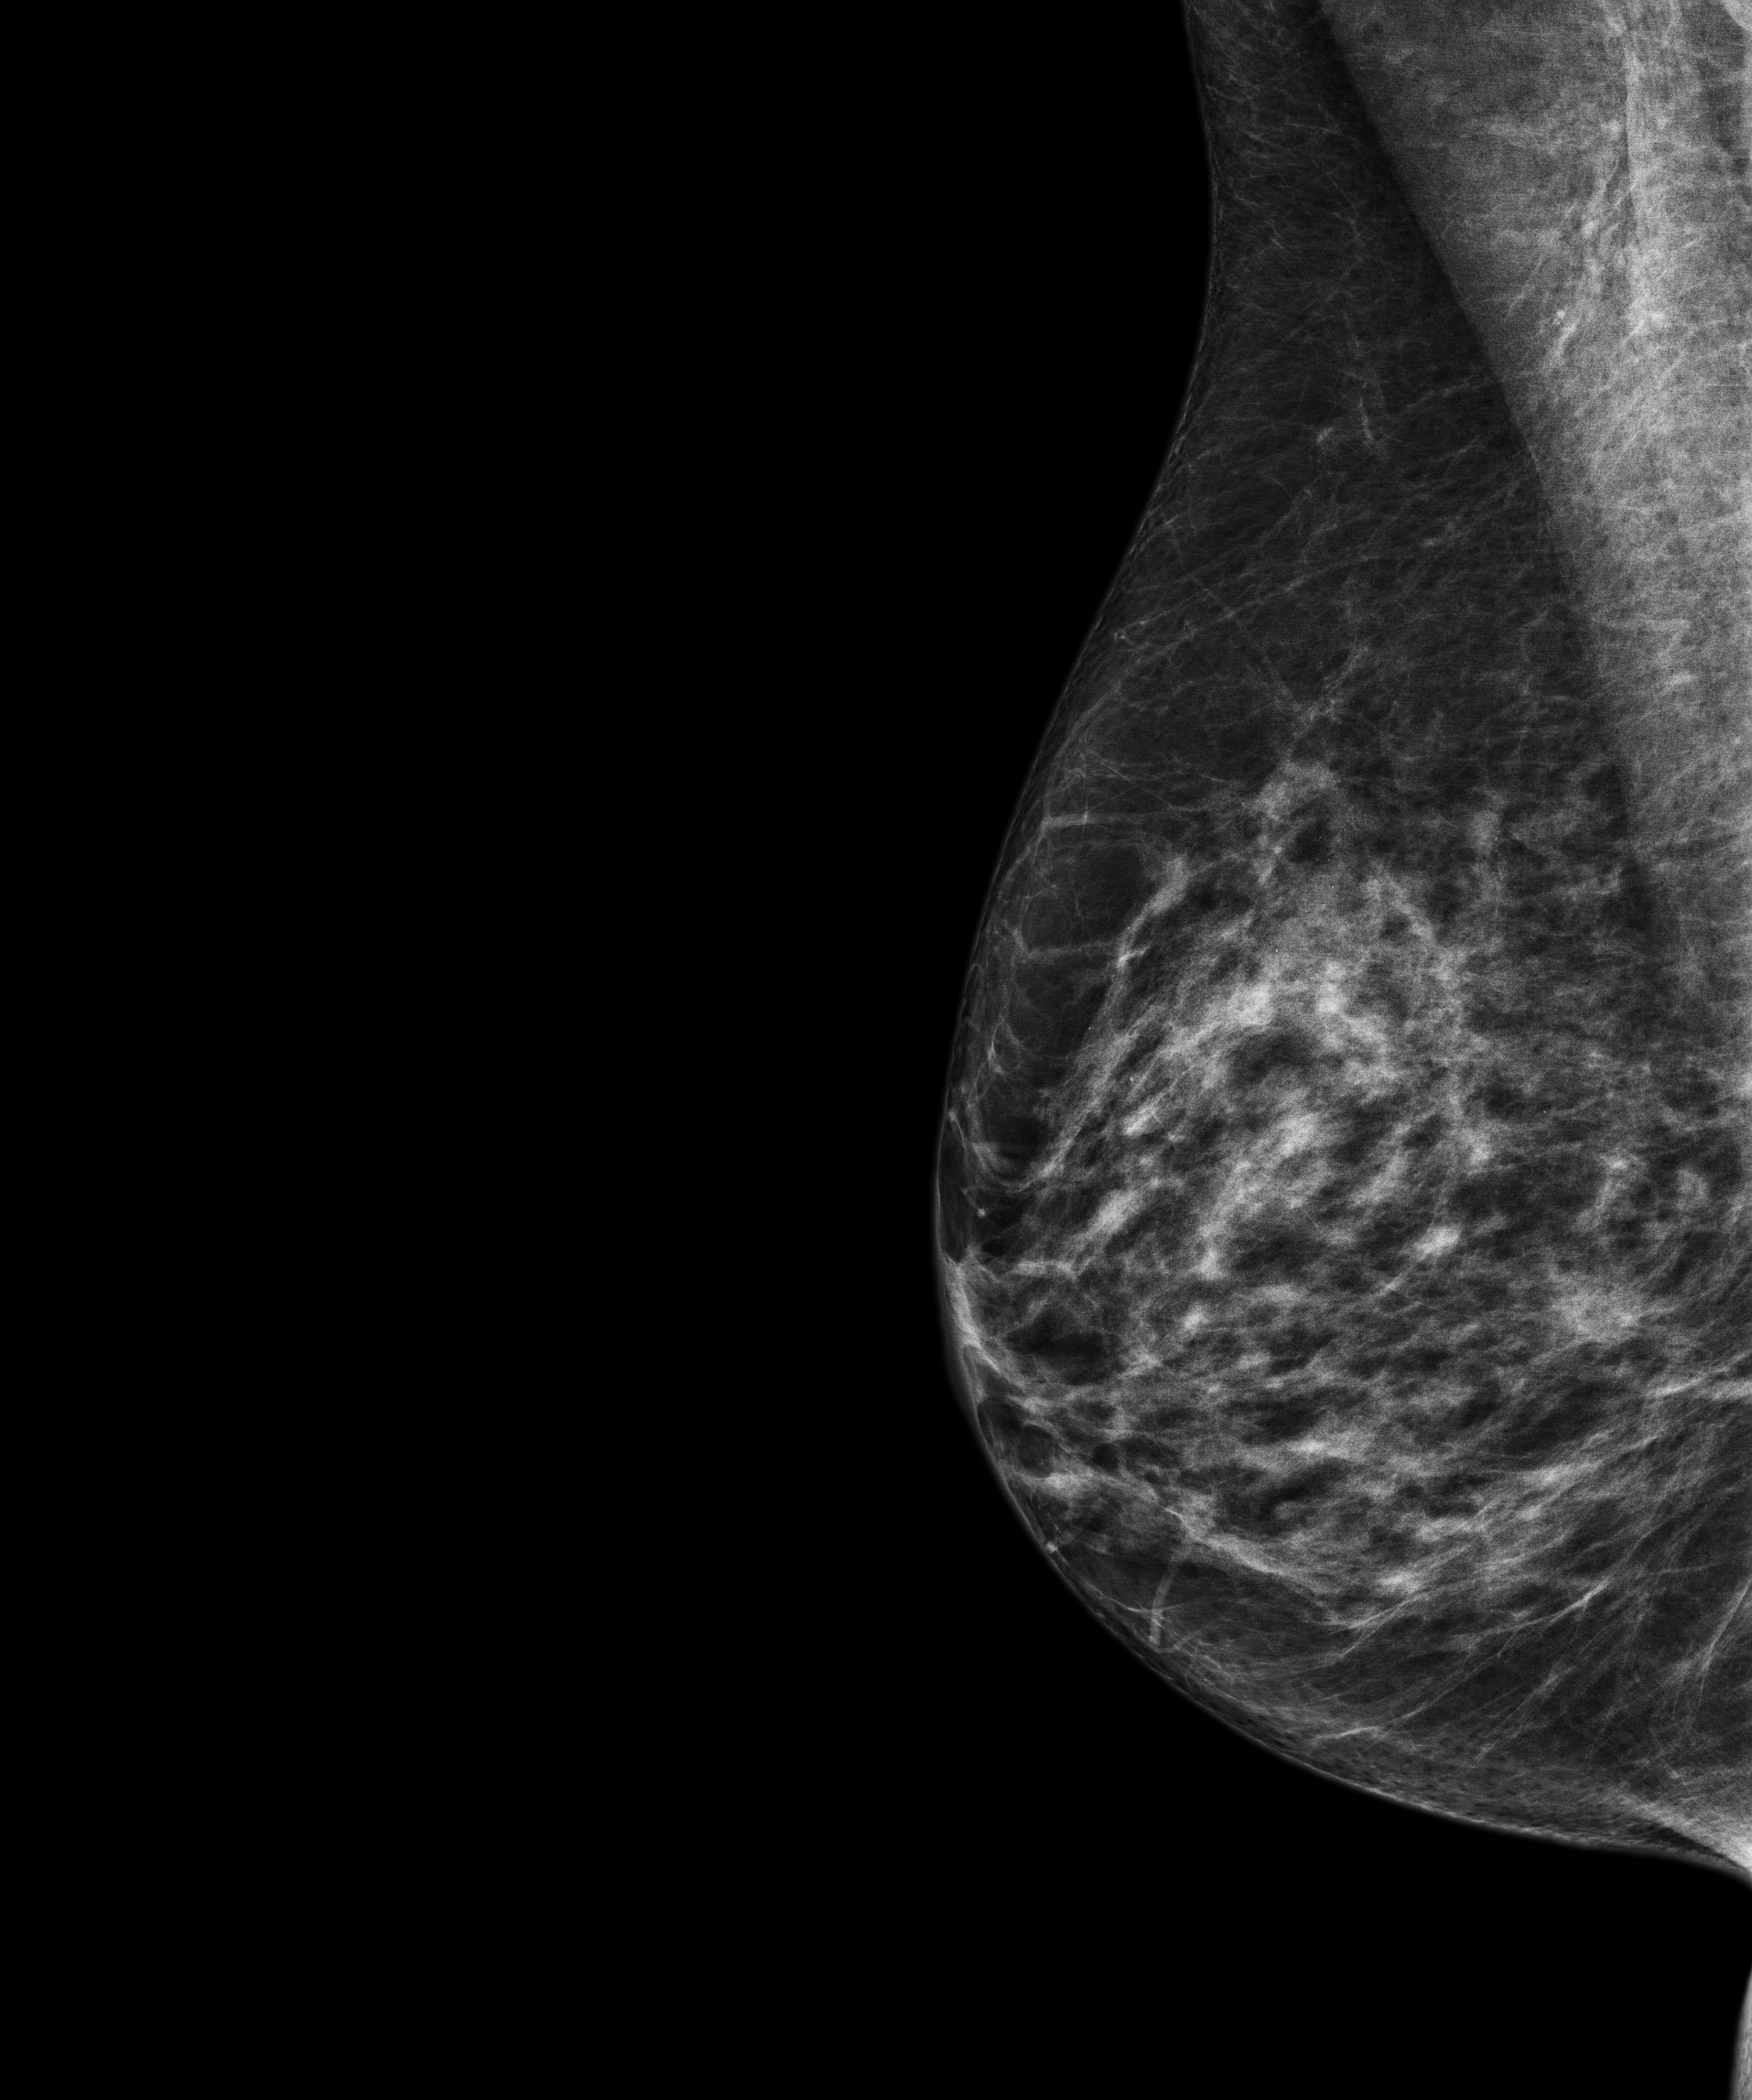
Annual screening mammography examination, compressed breast thickness 53 mm, system: Senographe Pristina. Patient: female, 59 years.
Image type: full-field digital mammogram. Breast: right. Projection: mediolateral oblique (MLO) view.